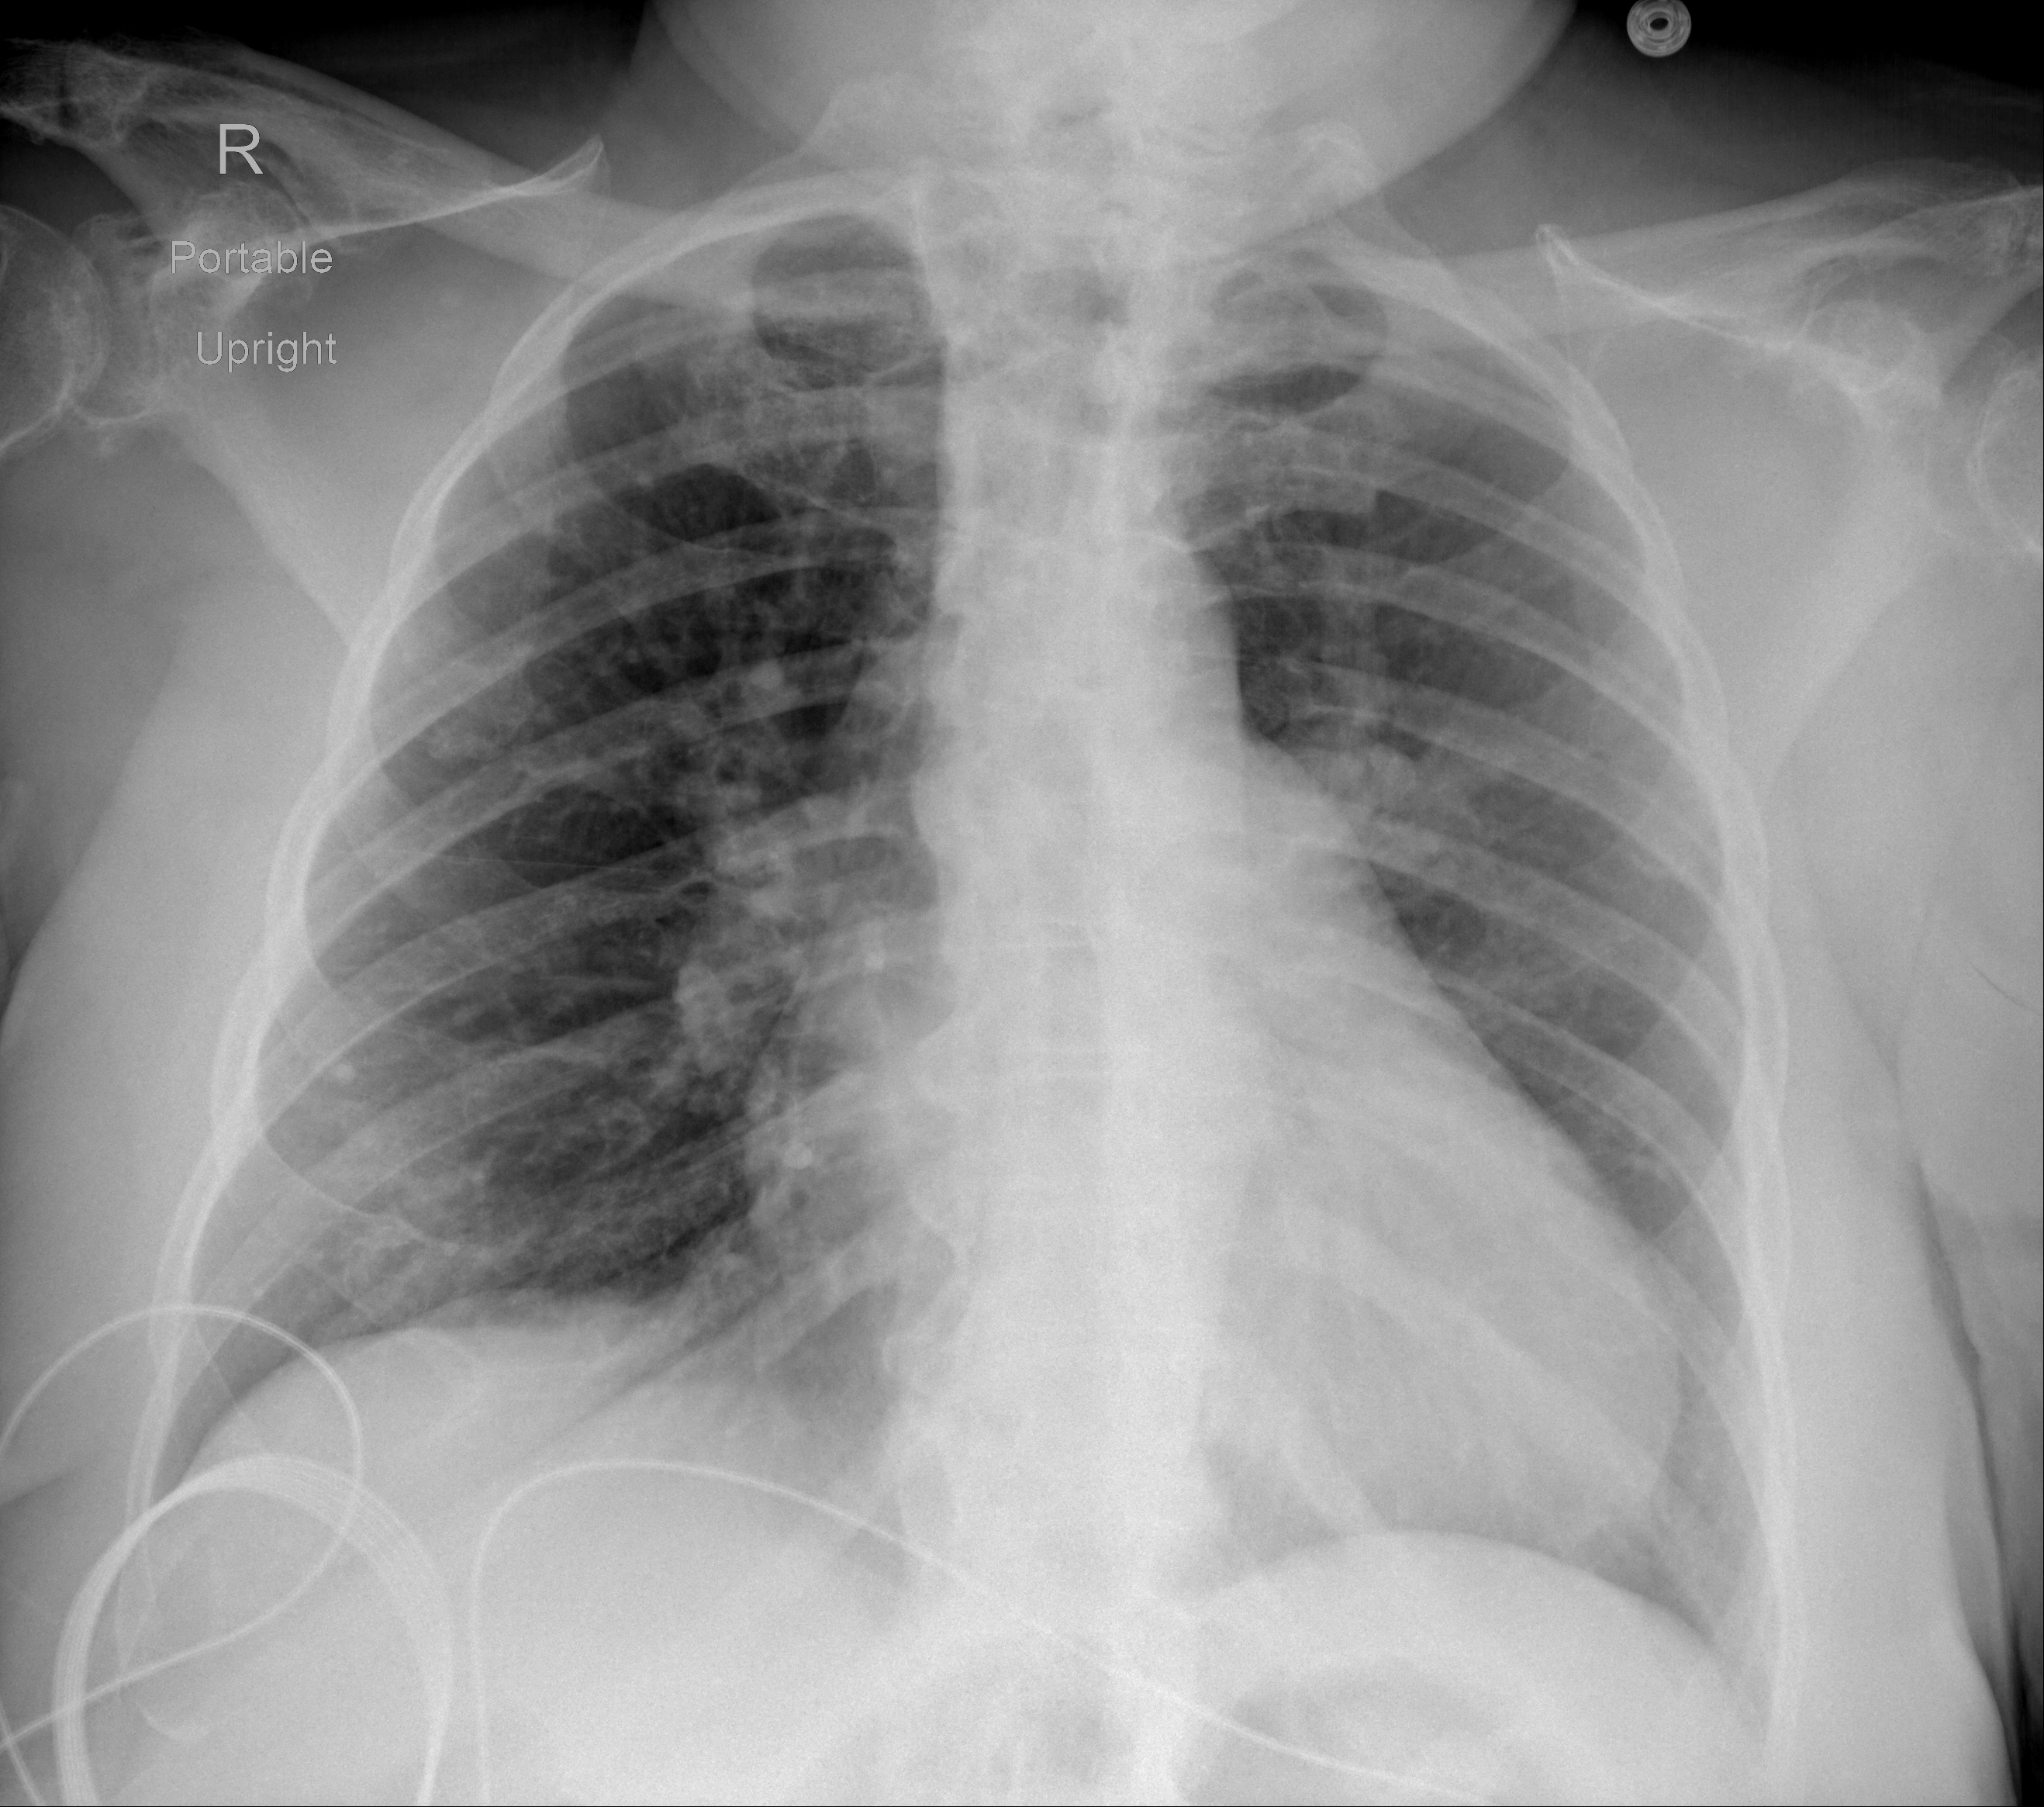
Chest X-ray (portable), AP projection. Female patient, age 69 years; imaged 1 day after the COVID-19 diagnosis.
Radiologist's key findings for this exam: The lungs are clear and without evidence of focal consolidation.